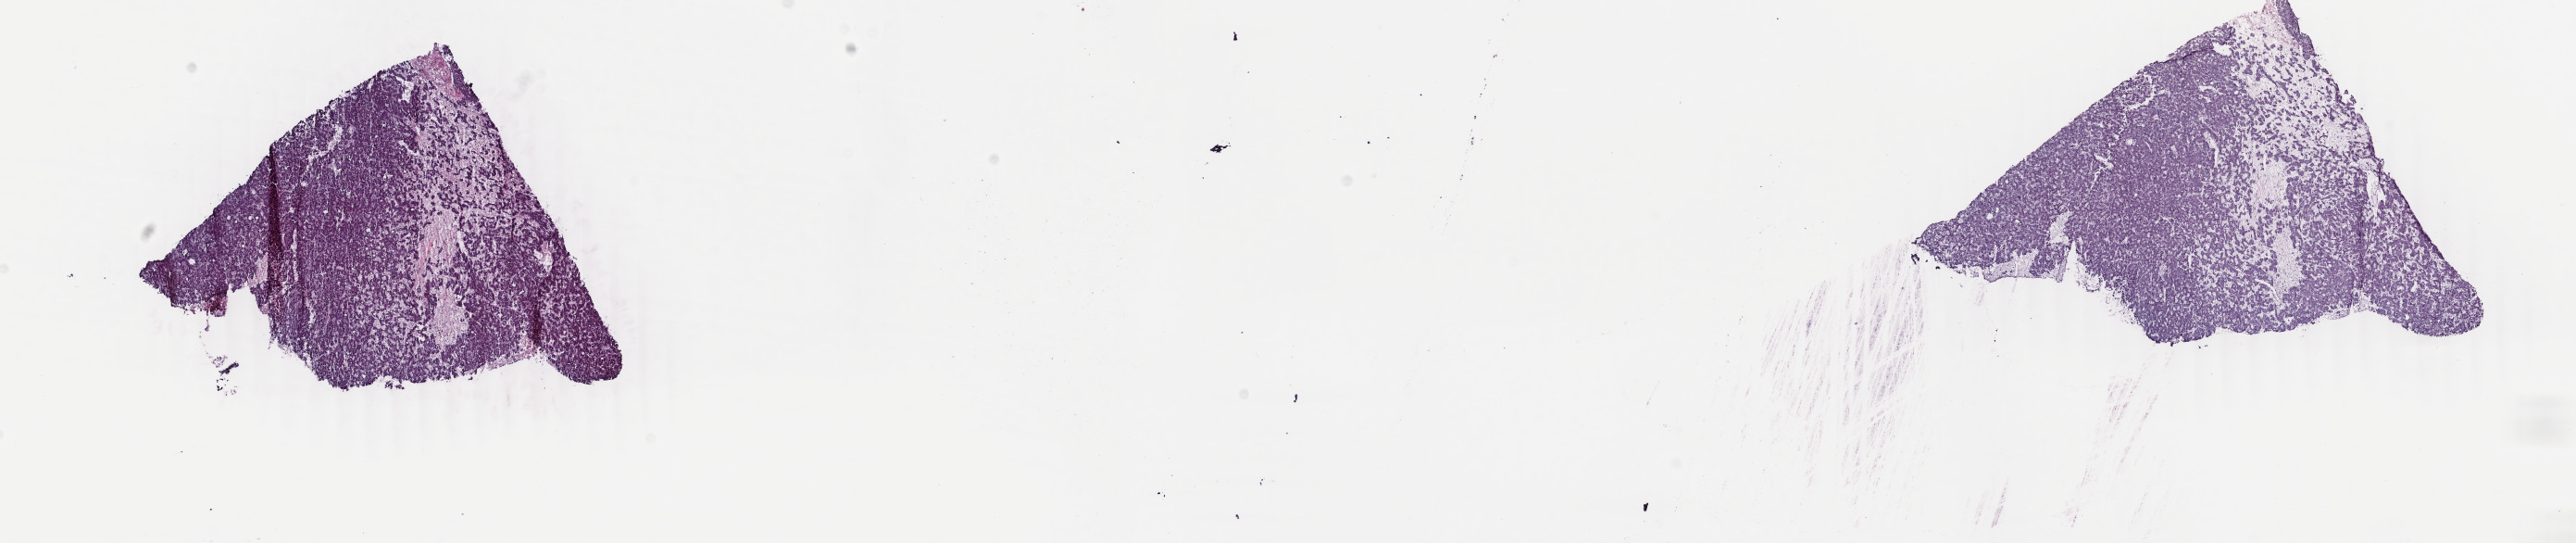
H&E whole-slide image — shown as a low-resolution overview of the whole scanned area (about 22.1 x 4.7 mm), frozen section from the bottom of the tissue portion, sample: primary tumour, liver. Male patient; age at initial diagnosis 81 years. Histologic grade: G1 (well differentiated). Composition of this section per pathologist review: tumour cells 90%, tumour nuclei 95%, normal cells 0%, stromal cells 10%, necrosis 0%. Infiltration values recorded for this section: lymphocyte infiltration 0%, monocyte infiltration 0%, neutrophil infiltration 0%.
Histologic diagnosis: Hepatocellular carcinoma, NOS.